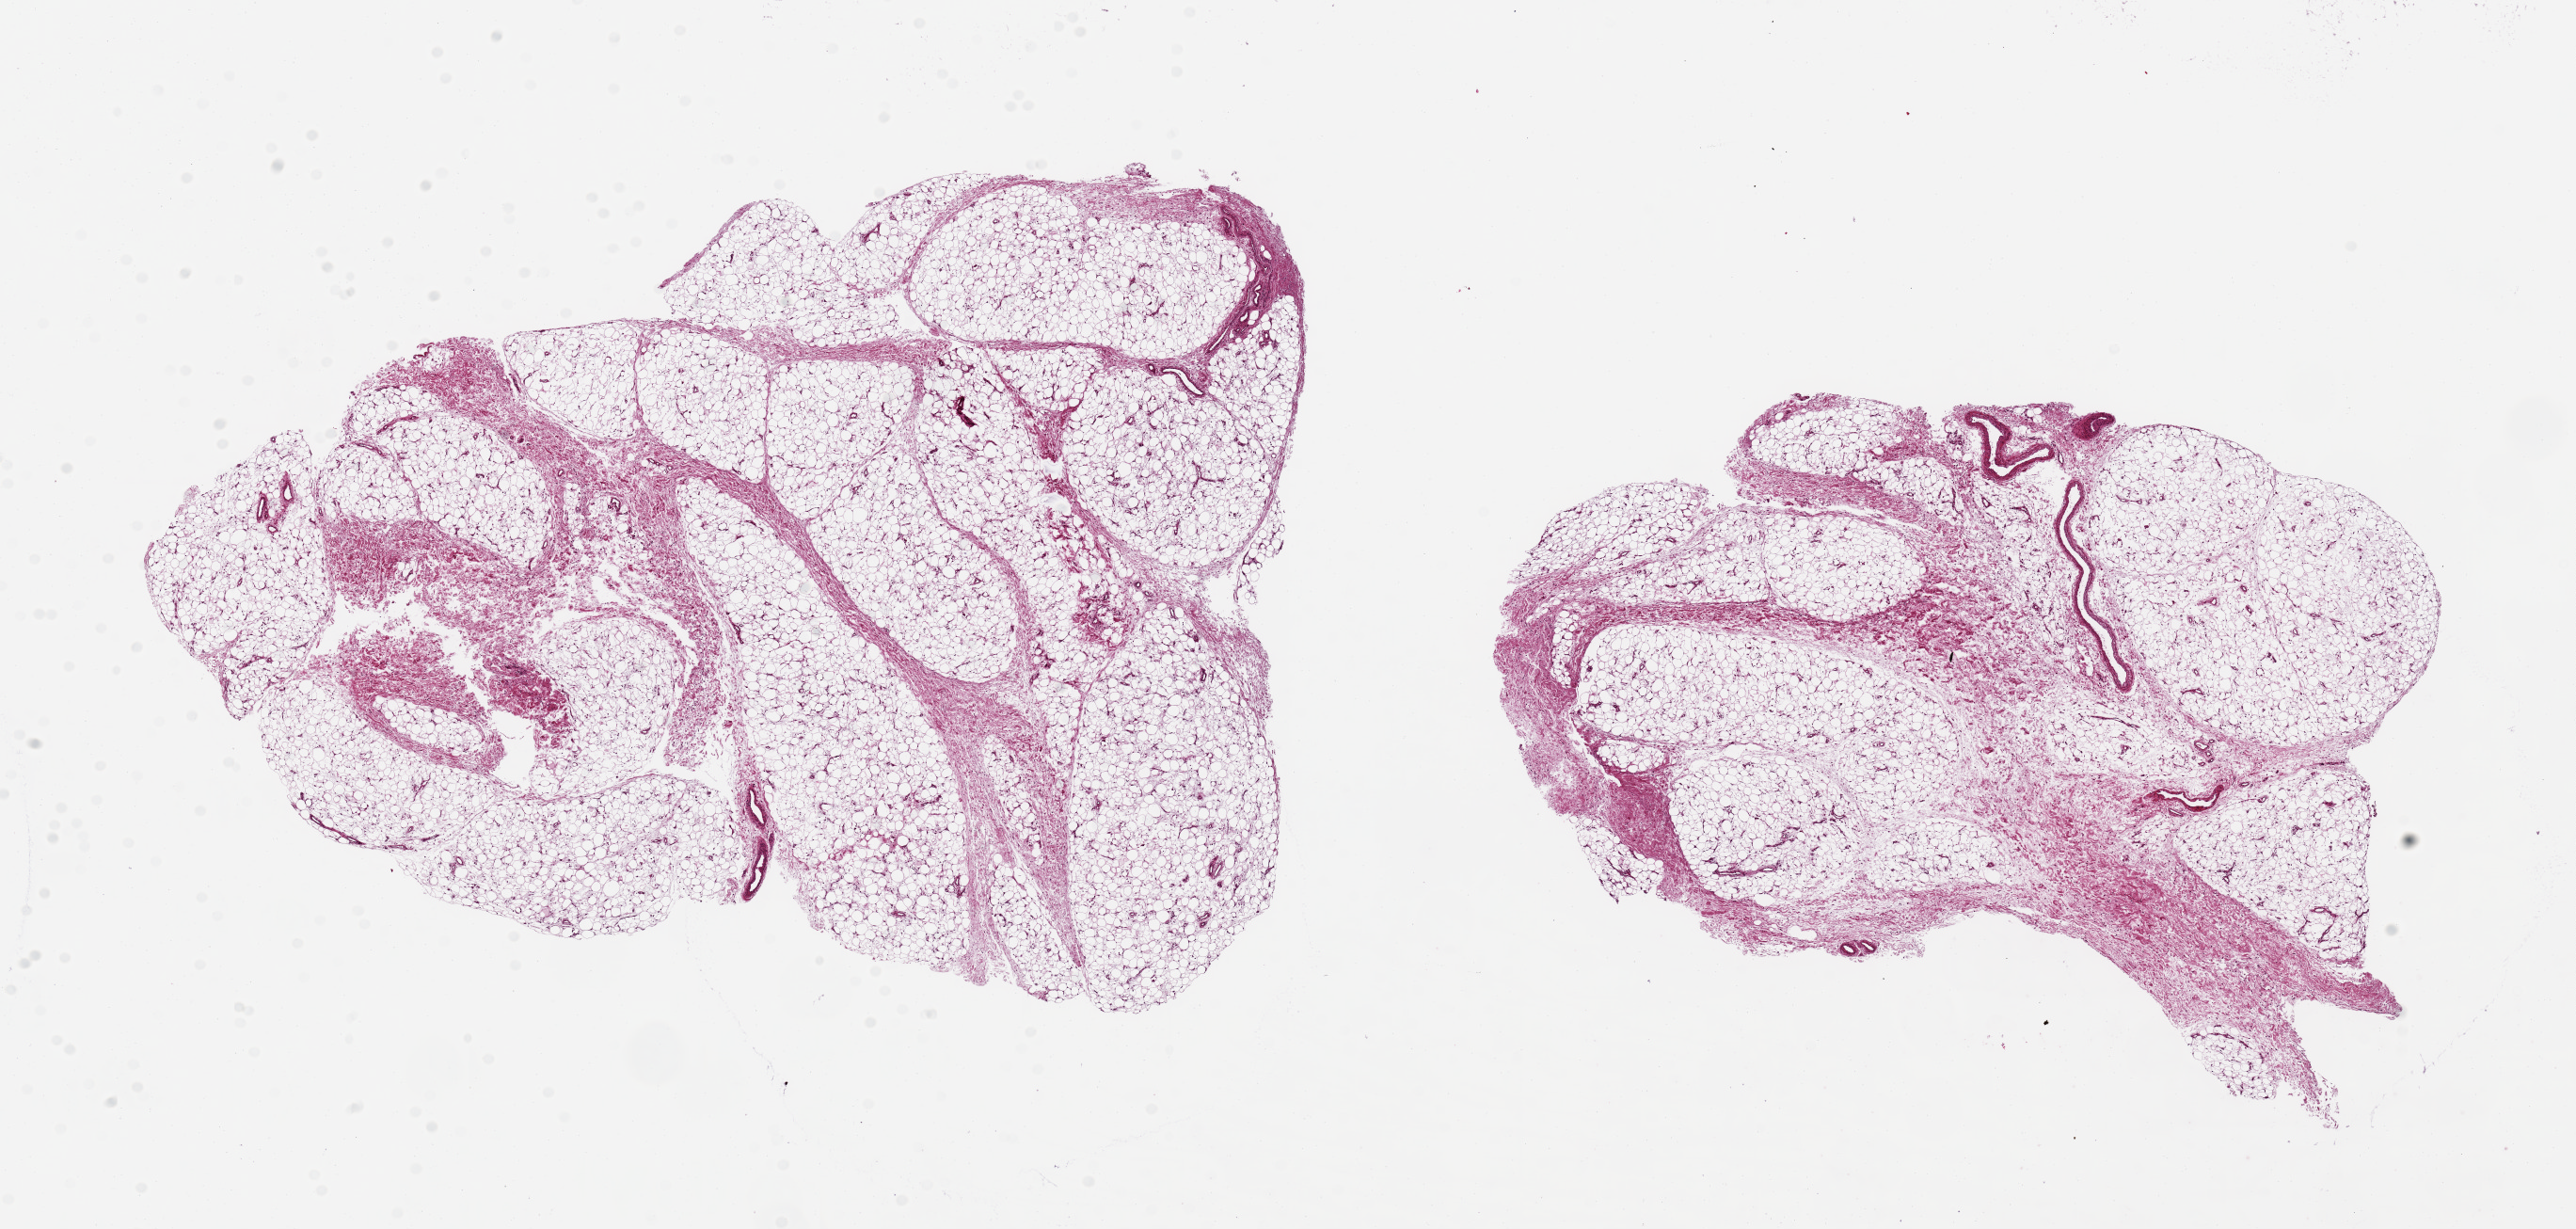
Hematoxylin and eosin (H&E) whole-slide image — low-resolution overview of the scanned area, about 21.7 x 10.3 mm. PAXgene-fixed paraffin-embedded (PFPE) section. Target tissue: adipose tissue. Donor tissue sample. Female donor.
• pathologist's review note for this sample: 2 ~8.5x6mm aliquots. Areas of under/poor fixation centrally